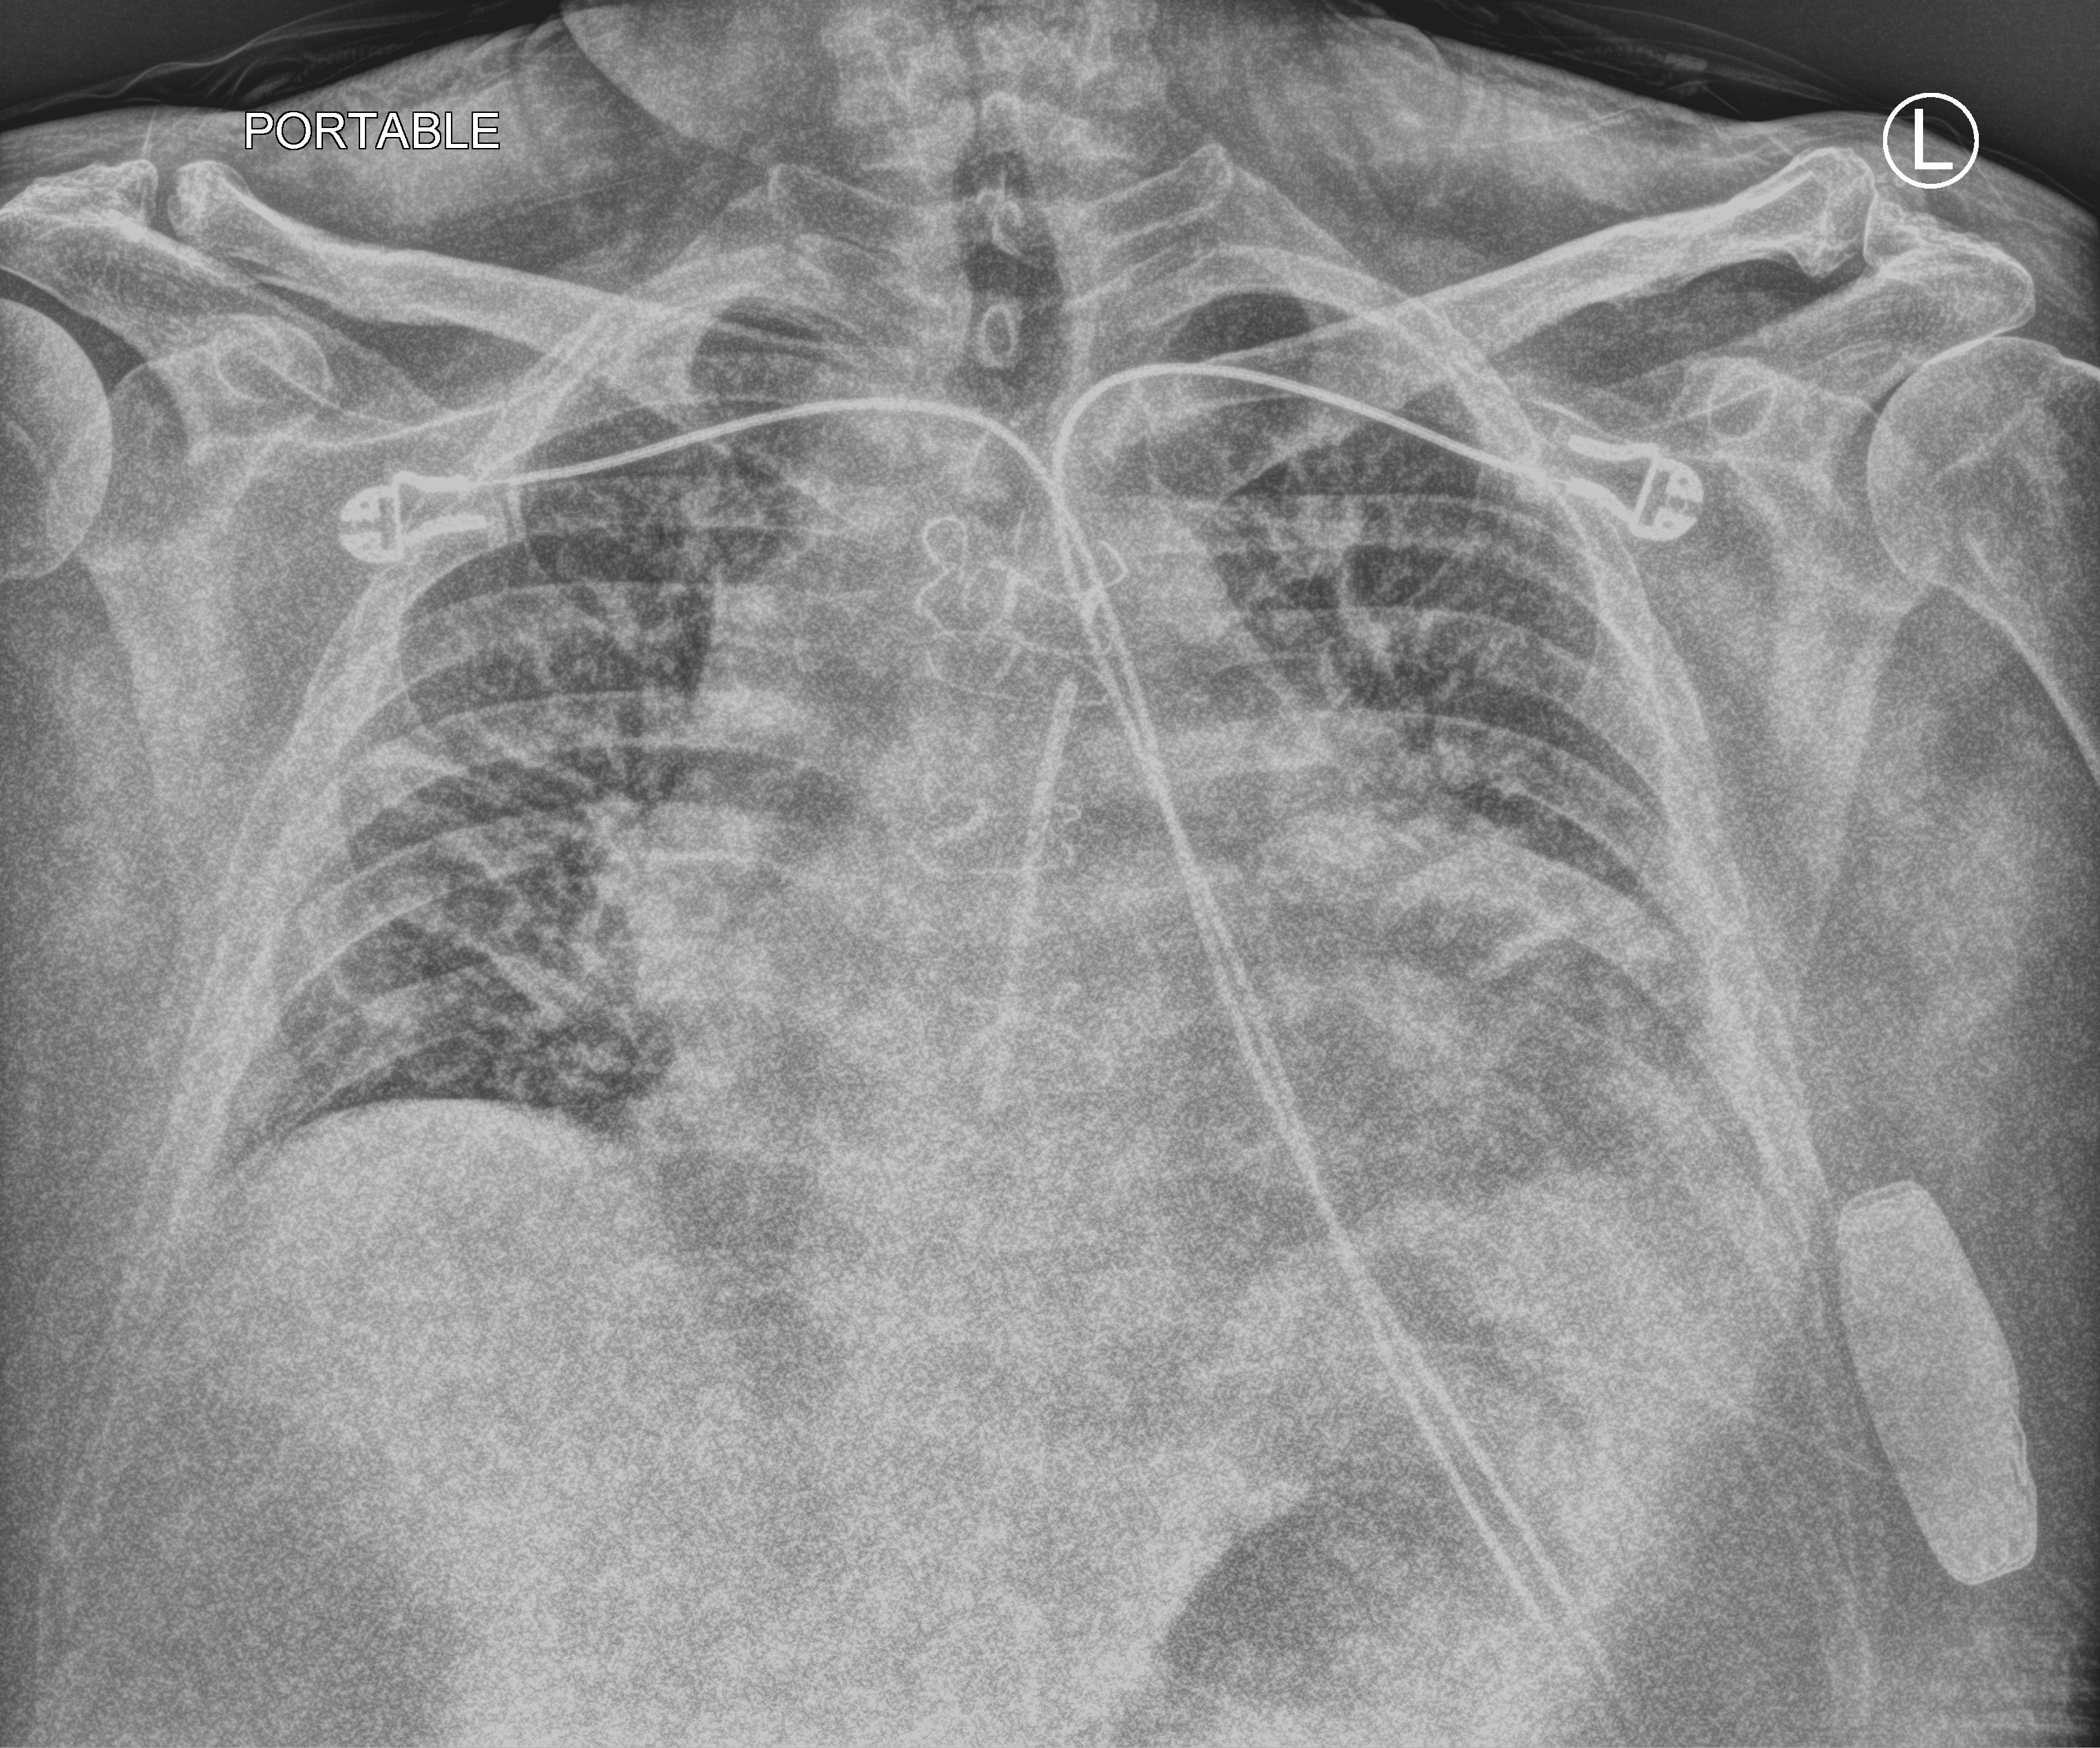
Chest X-ray (portable); anteroposterior (AP) projection. Male patient hospitalised with COVID-19, age 60–74 years.
Hospital-stay facts (about this admission, not read from this image; timing relative to this image not recorded): admitted to intensive care during this hospital stay: no; mechanically ventilated during this hospital stay: no.